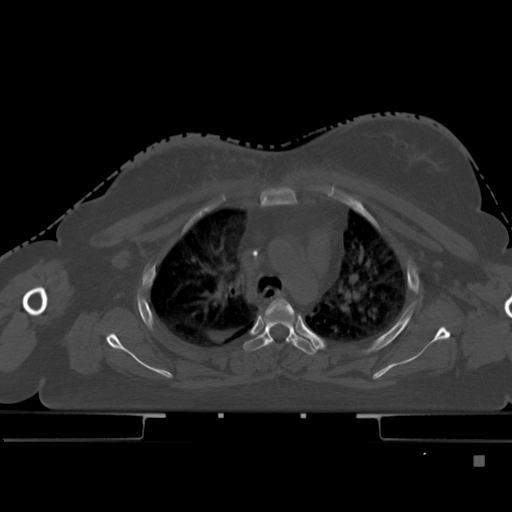
CT including the spine, one axial slice; slice 337 of 495 in the series (ordered by position); bone window (W 1800 / L 400 HU); 1.5 mm slice thickness; 512 × 512 image matrix, field of view 404 × 404 mm. Patient: female, 33 years. From the clinical record (not read from this slice): primary cancer: breast; vertebrae with lytic lesions (as recorded): T1.
Structures marked on this image (semi-automatic segmentation, software-assisted and operator-edited):
- T3 vertebra: bounding box [x1, y1, x2, y2] px = [267, 297, 294, 342]
- T4 vertebra: [244, 317, 320, 355]